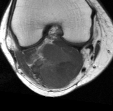
MRI of an extremity soft-tissue mass, one axial slice; position 16 of 45 along the scan axis; MR volume resampled by the dataset authors to the PET/CT grid (not the native acquisition matrix); 3.27 mm slice thickness; 113 × 111 image matrix, field of view 110 × 108 mm. Female patient. Case-level facts recorded for this patient, not image findings: histological type: liposarcoma; site of the primary tumour: right thigh.
Annotated regions visible in this slice (expert contour drawn on MRI and transferred to this co-registered scan by the dataset authors):
- gross tumour volume (mass): bounding box <28,42,77,88> (left, top, right, bottom; pixels)